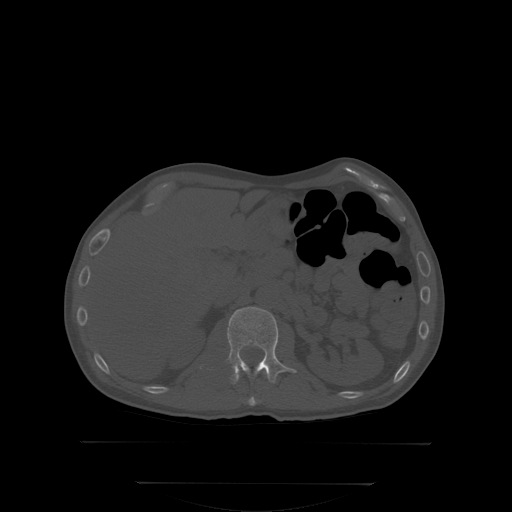
CT including the spine, one axial slice. Slice 156 of 350 in the series (ordered by position). Bone window (W 1800 / L 400 HU). 2.5 mm slice thickness. 512 × 512 image matrix, field of view 500 × 500 mm. Patient: male, 58 years. Case-level facts recorded for this patient, not image findings: primary cancer: prostate; vertebrae with lytic lesions (as recorded): L1.
Annotated regions visible in this slice (semi-automatically segmented with operator editing):
- L1 vertebra: bounding box [x1, y1, x2, y2] px = [227, 306, 291, 383]
- T12 vertebra: [247, 369, 266, 405]